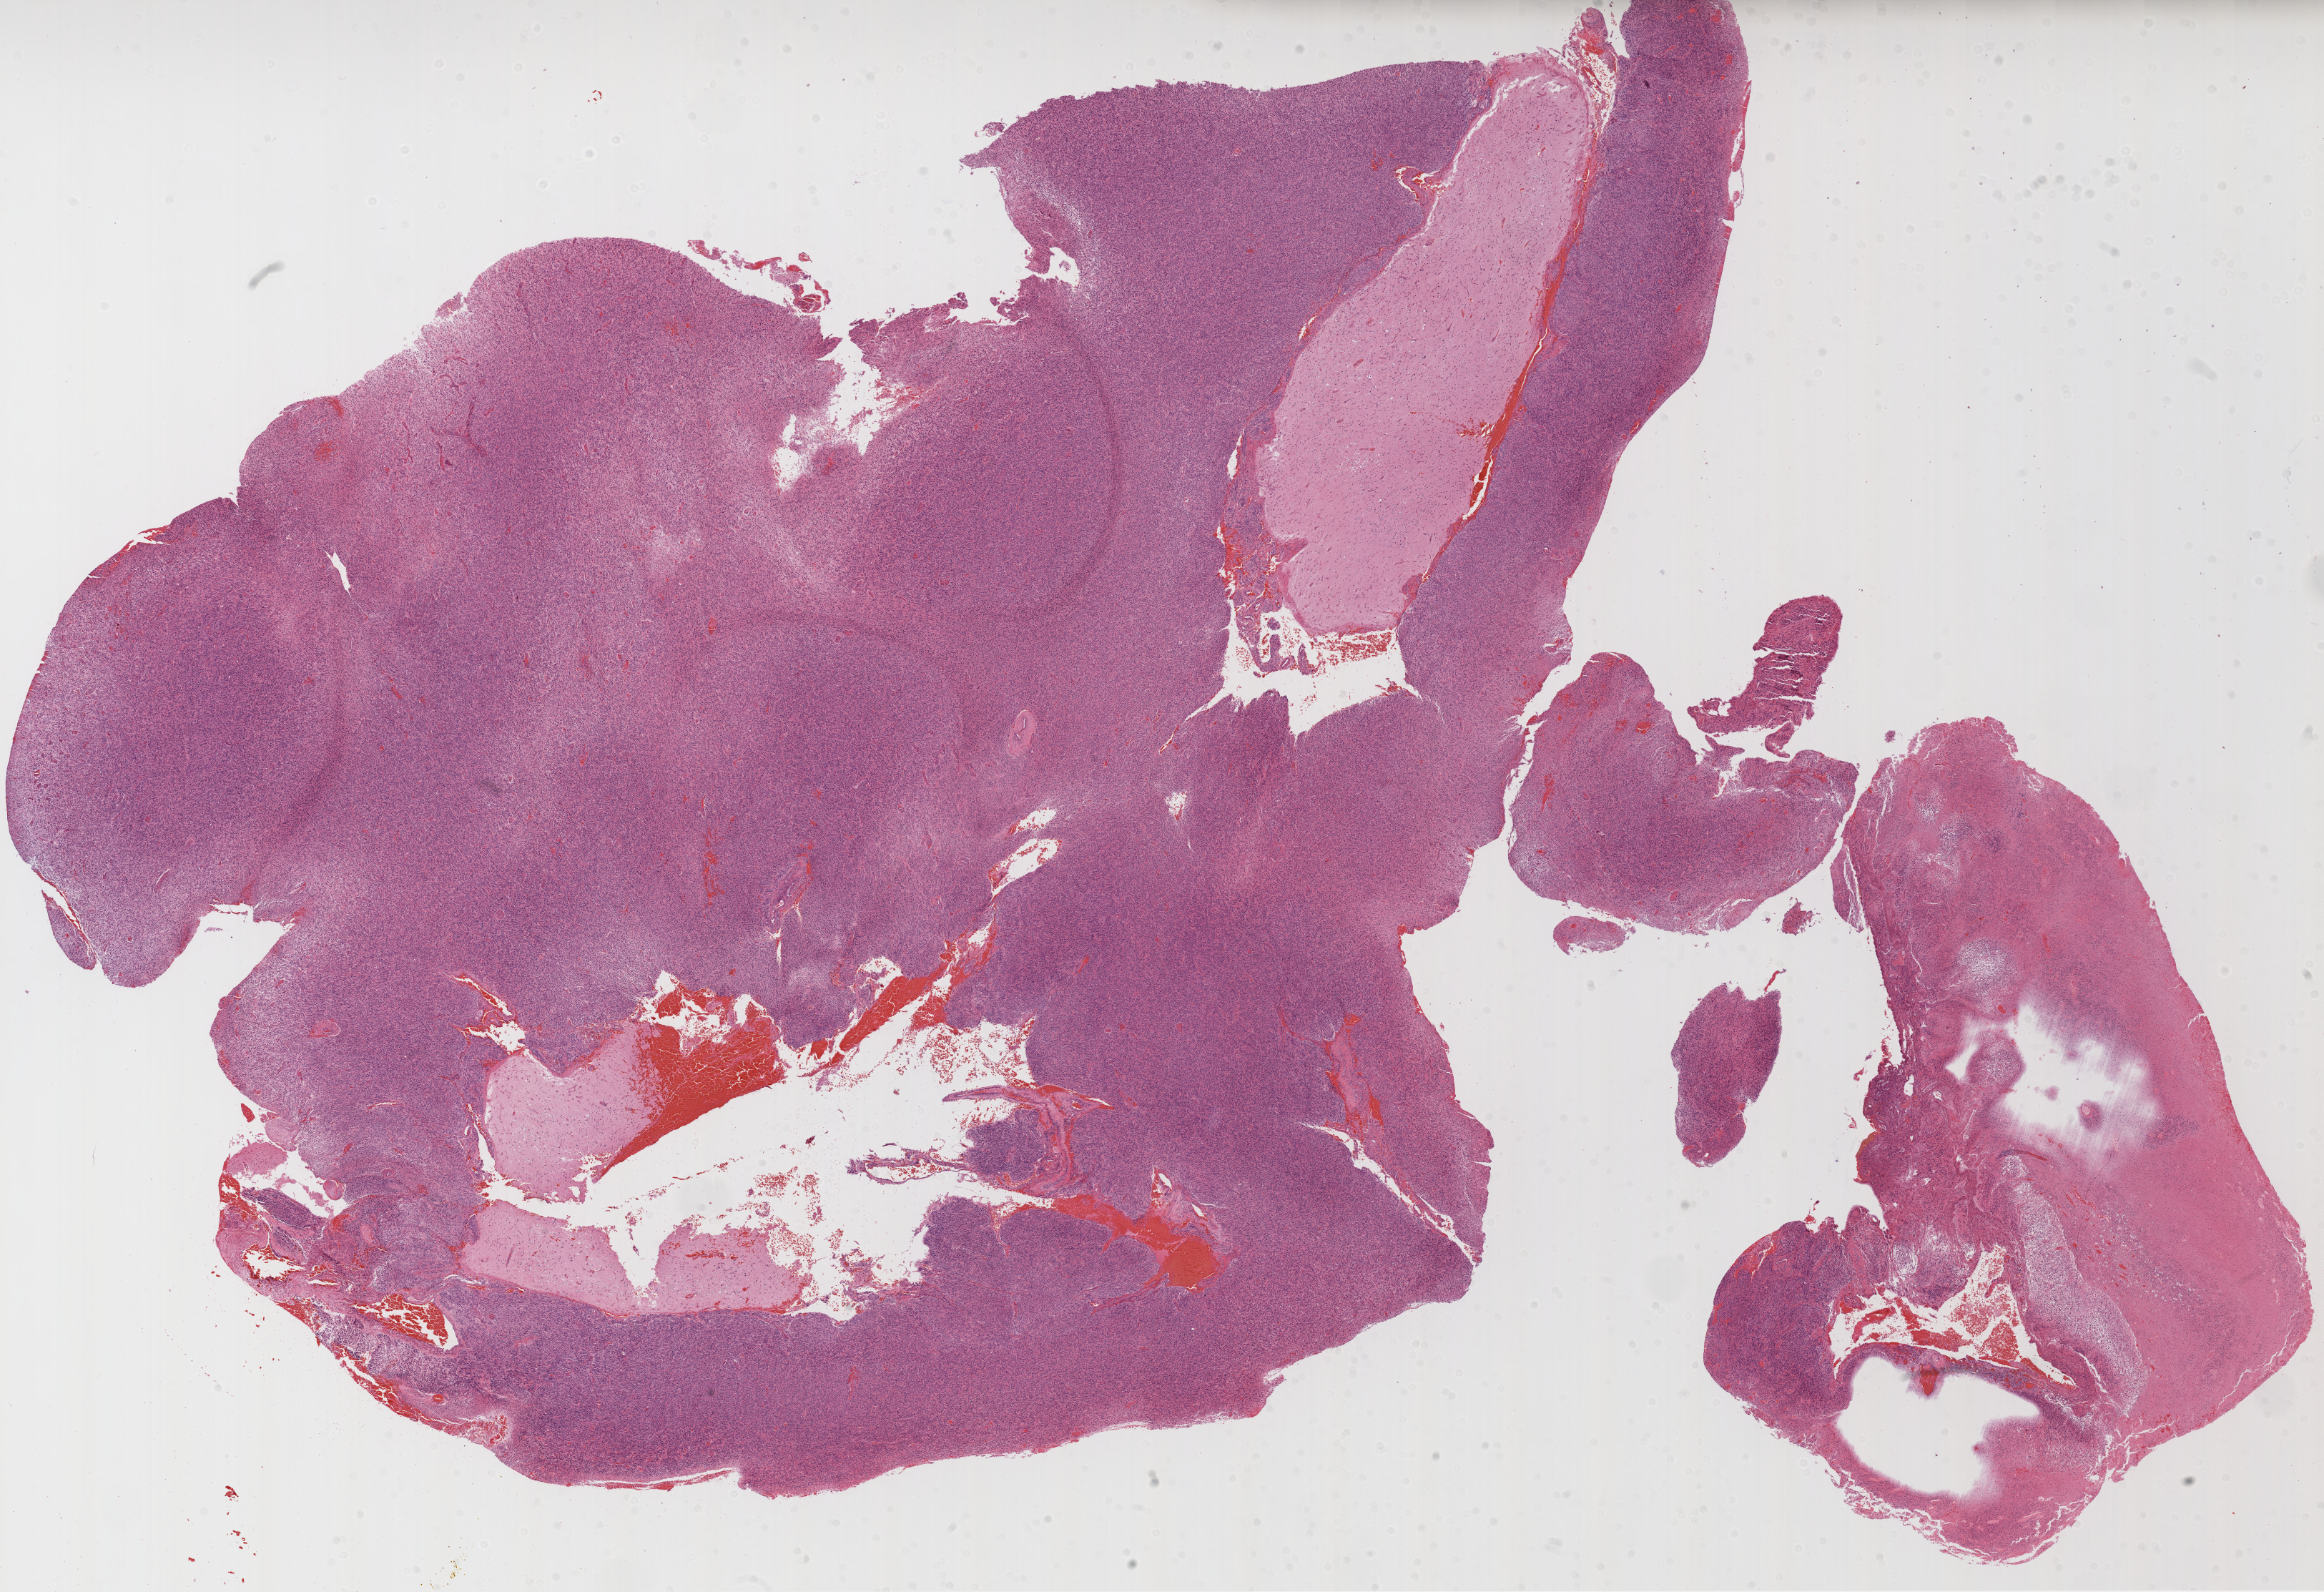
Whole-slide histology image, Hematoxylin and eosin (H&E) stained, whole scanned area (about 26.1 x 17.9 mm) shown as a low-resolution overview. Formalin-fixed paraffin-embedded (FFPE) diagnostic section. Primary tumour sample from the brain. Patient: male, age at initial diagnosis 76 years.
- pathologic diagnosis: Glioblastoma